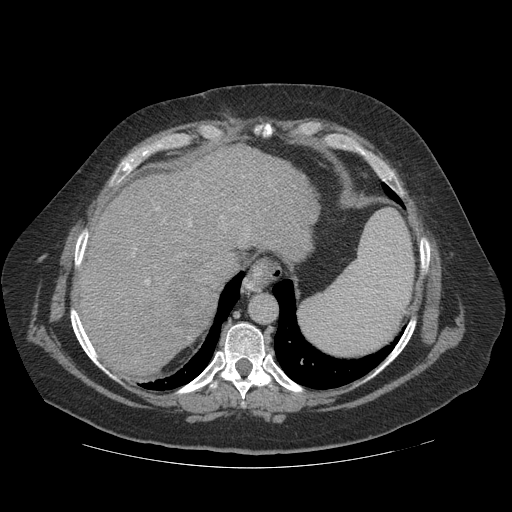
Contrast-enhanced abdominal CT (liver protocol), one axial slice; slice 94 of 121 in the series (ordered by position); reconstruction kernel STANDARD; soft-tissue window (W 400 / L 40 HU); 2.5 mm slice thickness; 512 × 512 image matrix, field of view 420 × 420 mm. Case-level facts recorded for this patient, not image findings: diagnosis: hepatocellular carcinoma (patient treated with transarterial chemoembolisation; whether this scan precedes or follows treatment is not stated here); TNM stage (as recorded): Stage-IIIA; Child-Pugh class: A; tumour differentiation: well differentiated.
Outlined on this slice (semi-automatically segmented with operator editing):
- abdominal aorta: bounding box <251,296,277,324> (left, top, right, bottom; pixels)
- liver parenchyma outside the tumour (the mass and vessels are separate outlines, so this box may not span the whole liver): <74,145,320,376>
- mass: <163,278,216,338>
- liver vessels: <132,176,271,285>